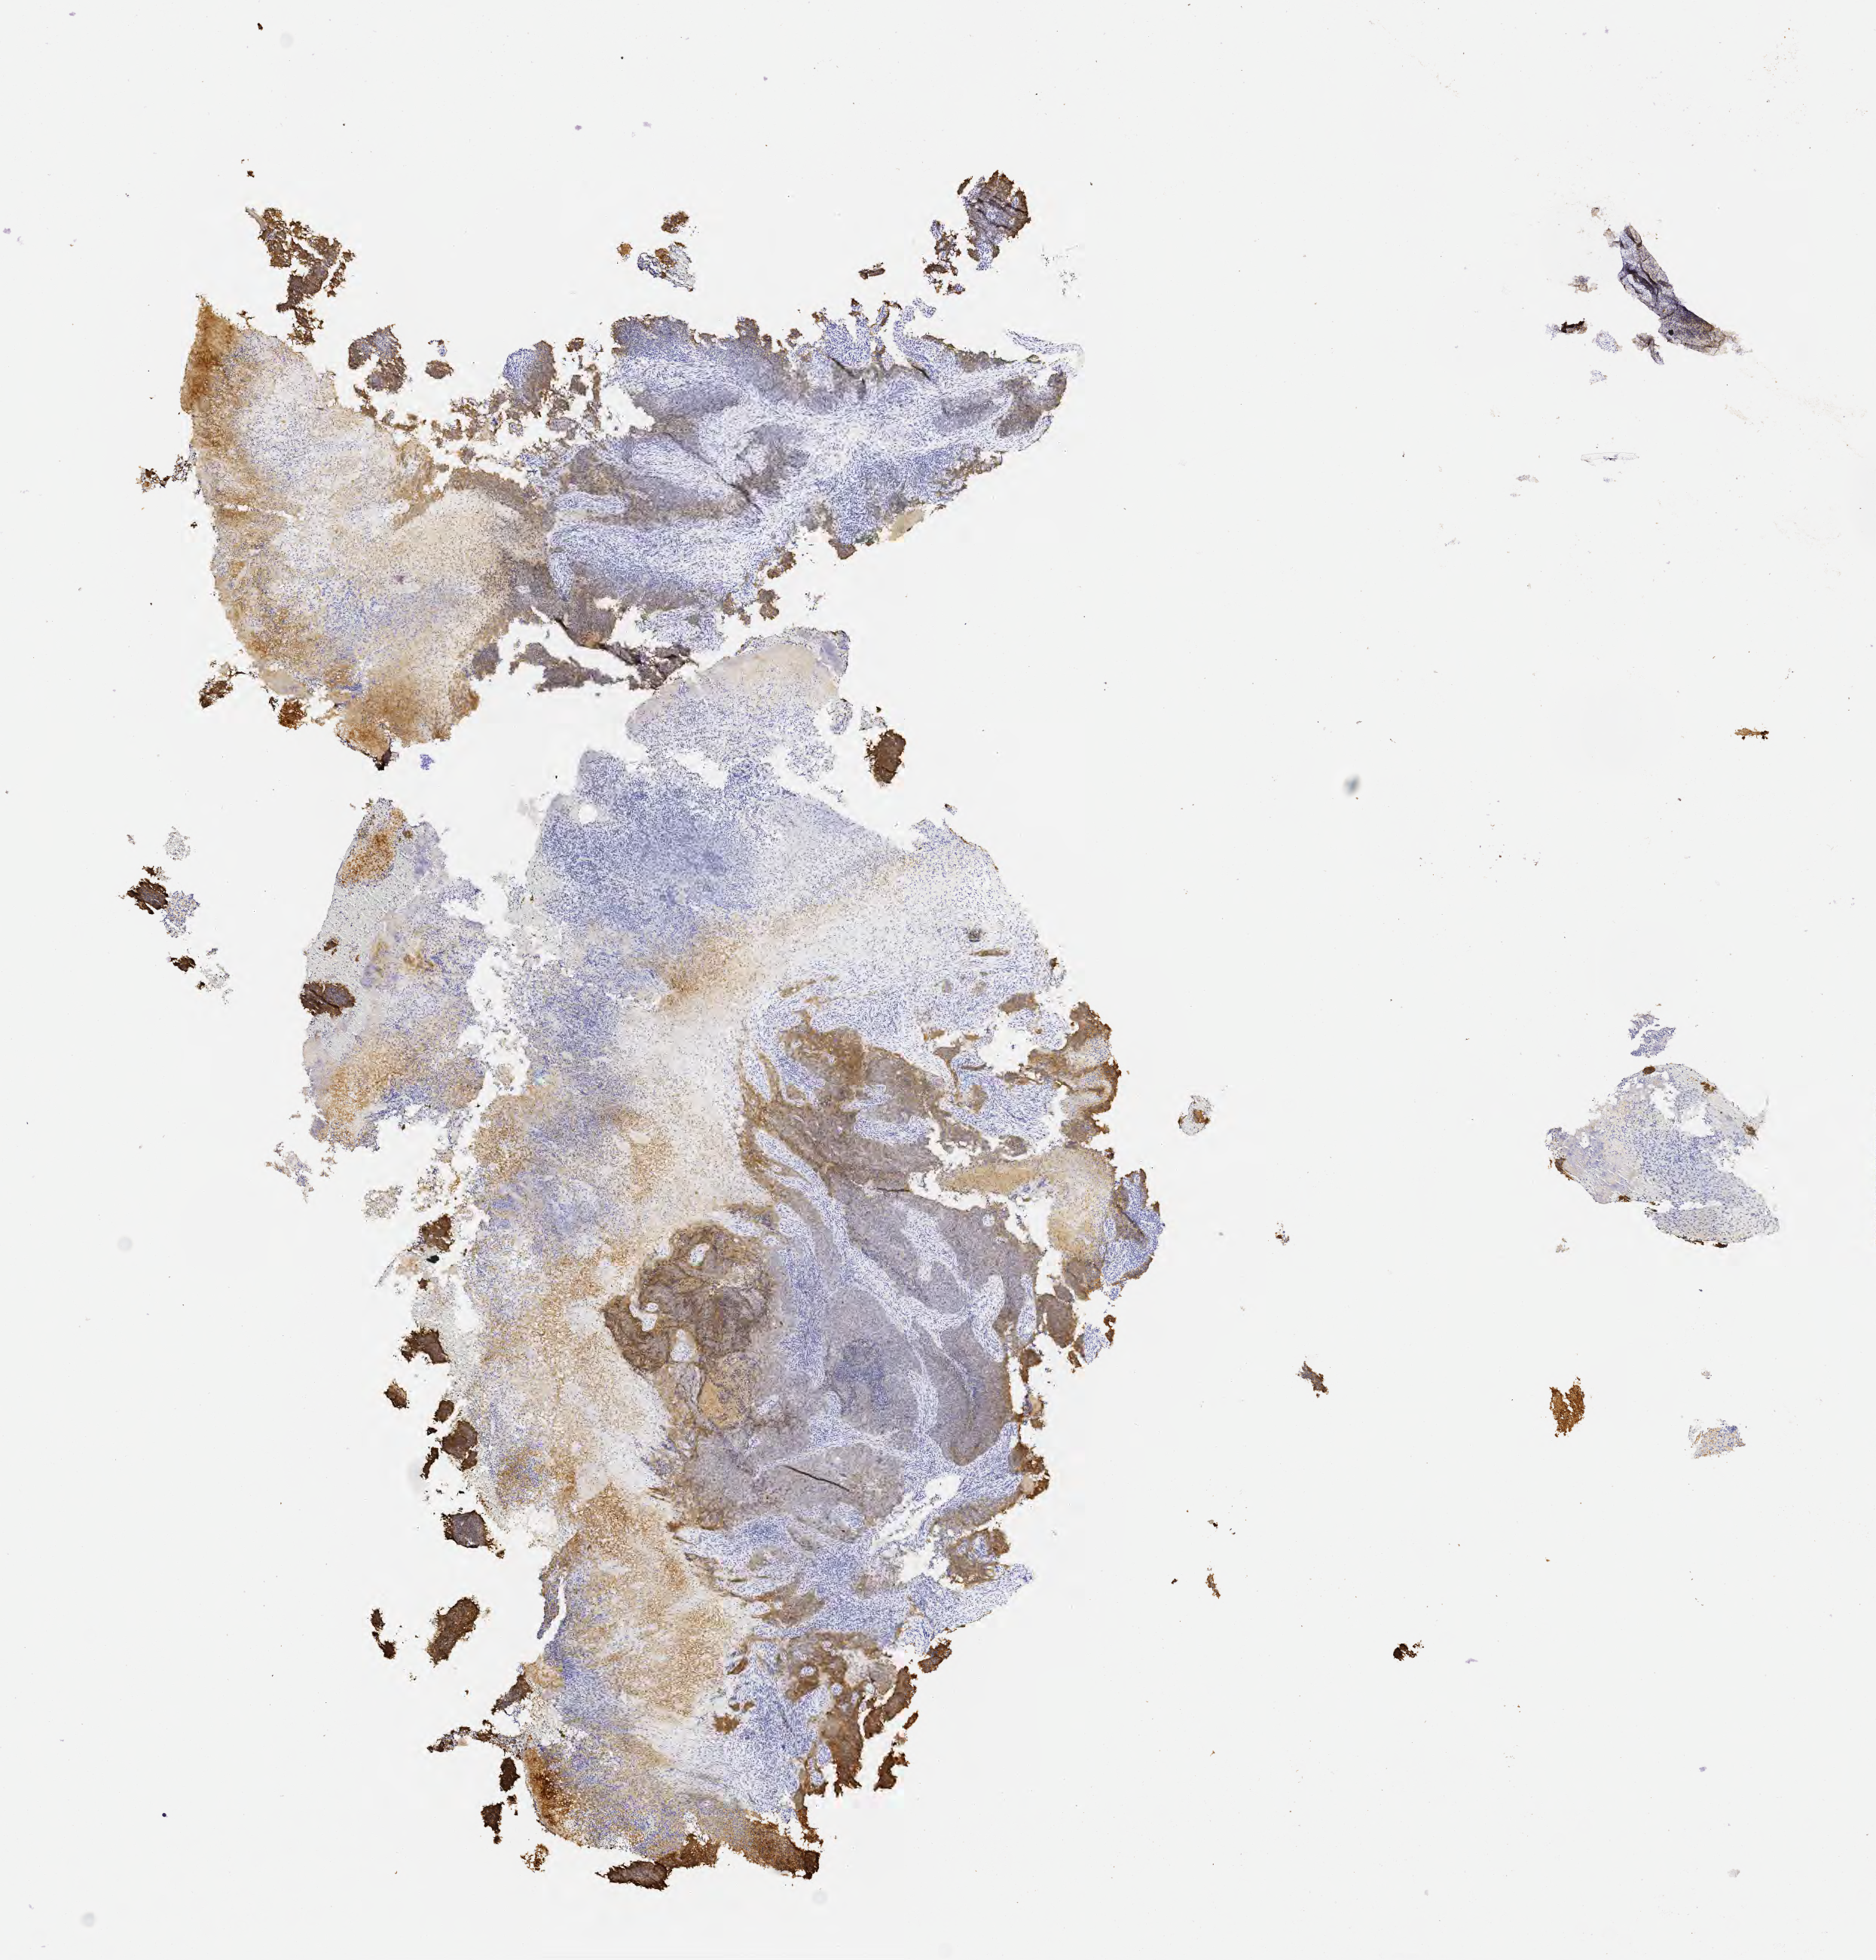
IHC for MOC-31 (anti-EpCAM), whole-slide image, whole scanned area (about 10.1 x 10.5 mm) shown as a low-resolution overview; tumor tissue; anatomic site: cervix. Female patient, age 65 years.
Diagnosis: Squamous cell carcinoma, large cell, nonkeratinizing, NOS.